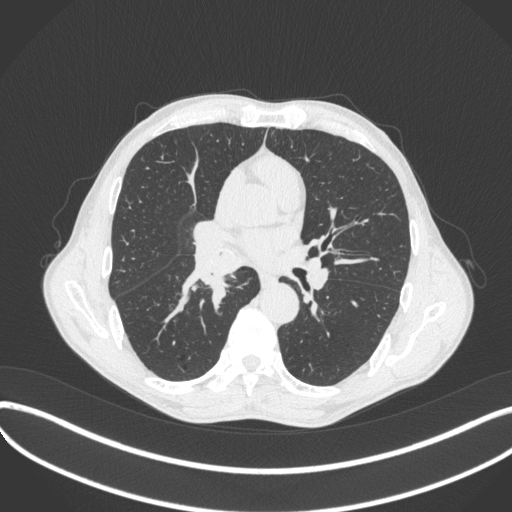
Chest CT, one axial slice; position 232 of 481 along the scan axis; lung window (W 1500 / L -600 HU); 512 × 512 image matrix, field of view 400 × 400 mm. Male patient, age 65 years. Case-level facts recorded for this patient, not image findings: clinical TNM (as recorded): T2a N0 M0; histopathological grade: G2.
Structures marked on this image (bounding box drawn by a radiologist):
- lung tumour (recorded histology: squamous cell carcinoma): bounding box [x1, y1, x2, y2] px = [187, 240, 242, 307]